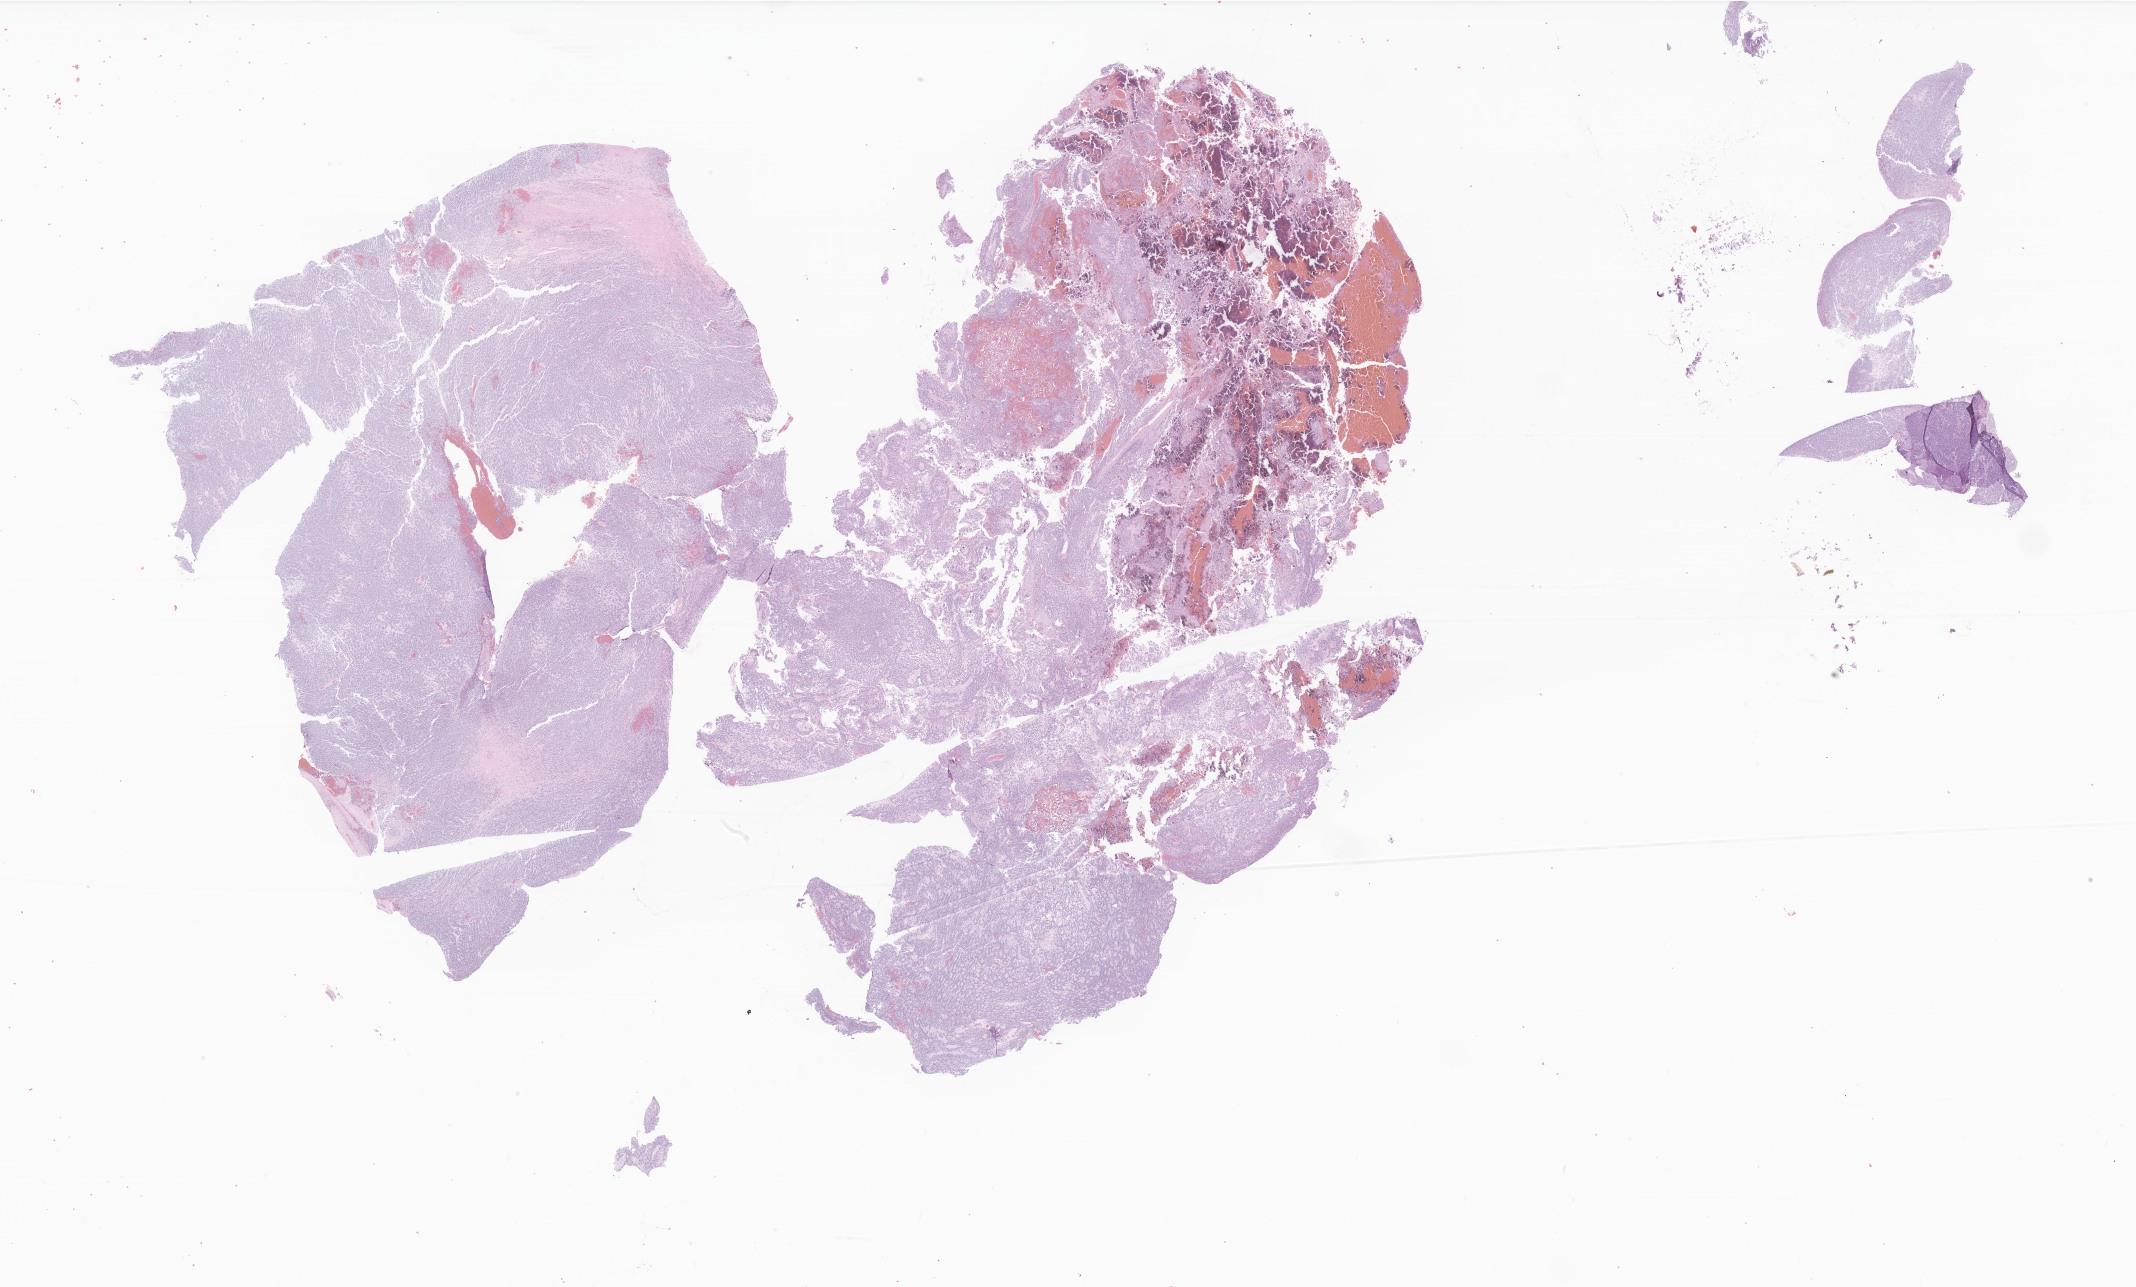
H&E whole-slide image of tumor tissue from the brain stem, a low-resolution overview of the entire scanned area, about 36.0 x 21.7 mm. Formalin-fixed paraffin-embedded section. Female patient, age 88 months.
Diagnosis: Medulloblastoma, NOS.